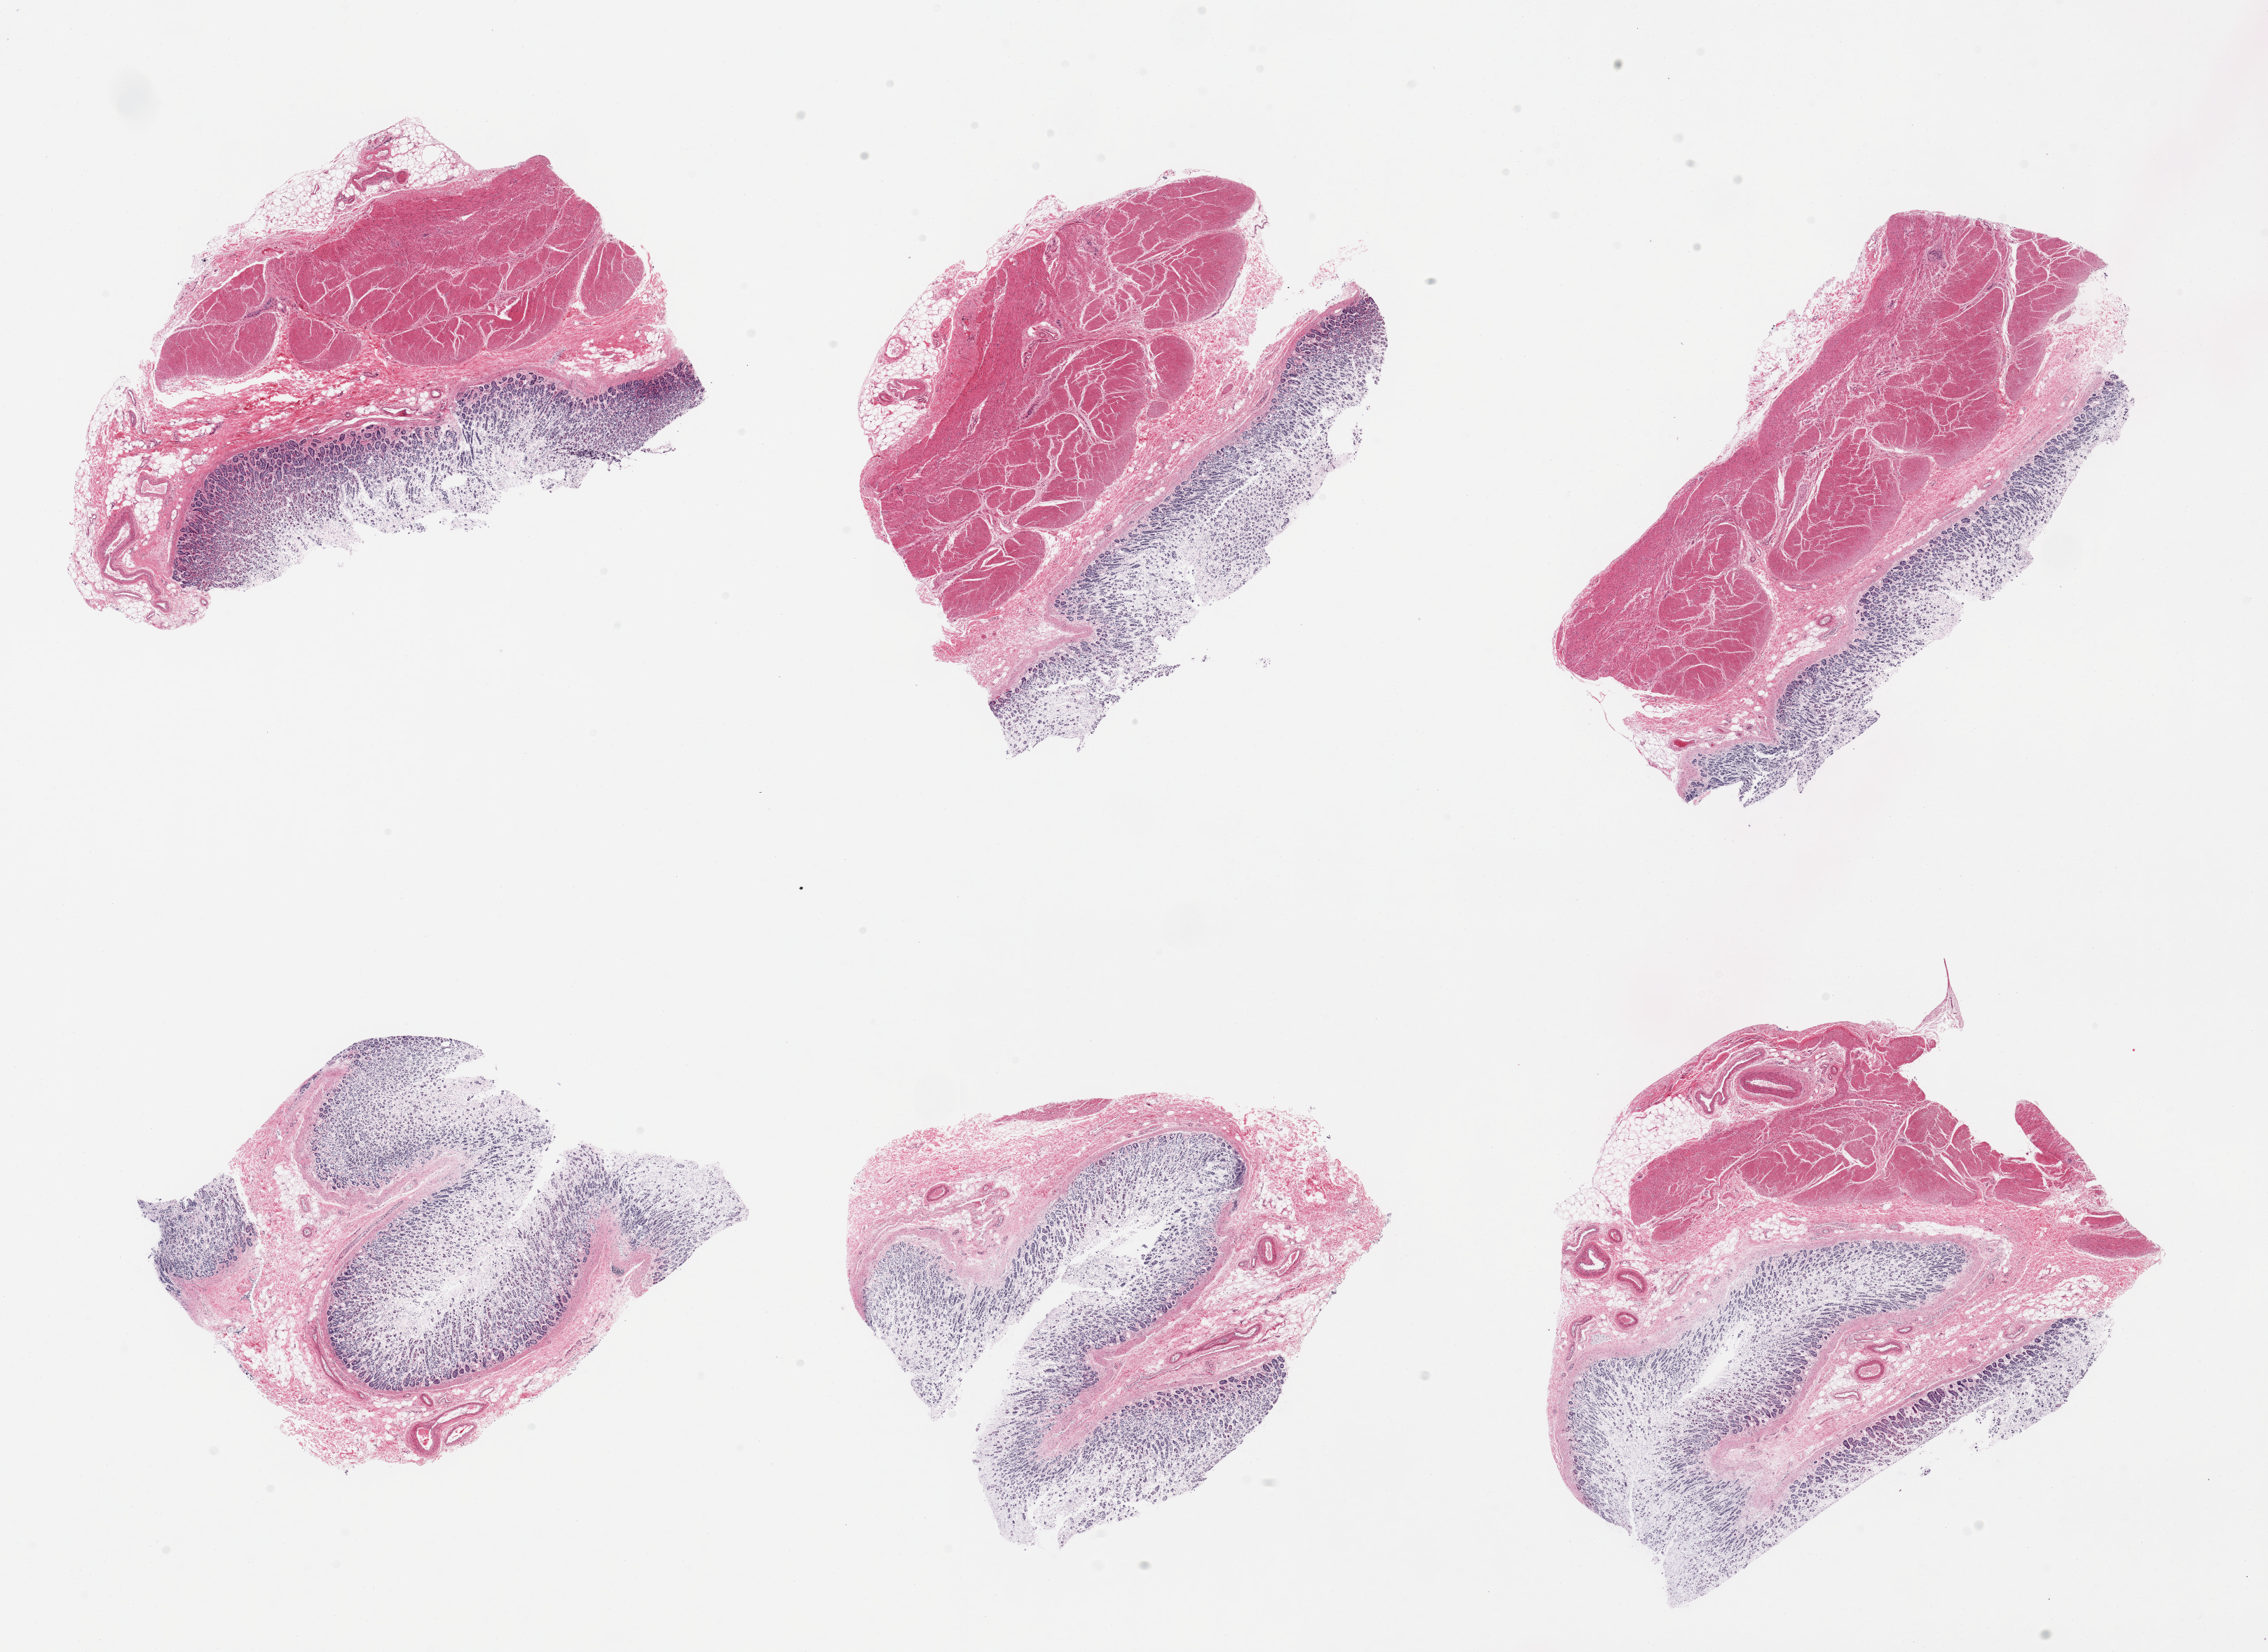
Whole-slide image, hematoxylin and eosin (H&E) stain, brightfield — a low-resolution overview of the entire scanned area, about 25.6 x 18.6 mm (slide scanned at 20x). PAXgene-fixed, paraffin-embedded tissue. Section of stomach (target tissue). Donor tissue sample. Donor: female.
Reviewer comment on this tissue sample: 6 pieces; four are full thickness, two are mucosa/submucosa only.